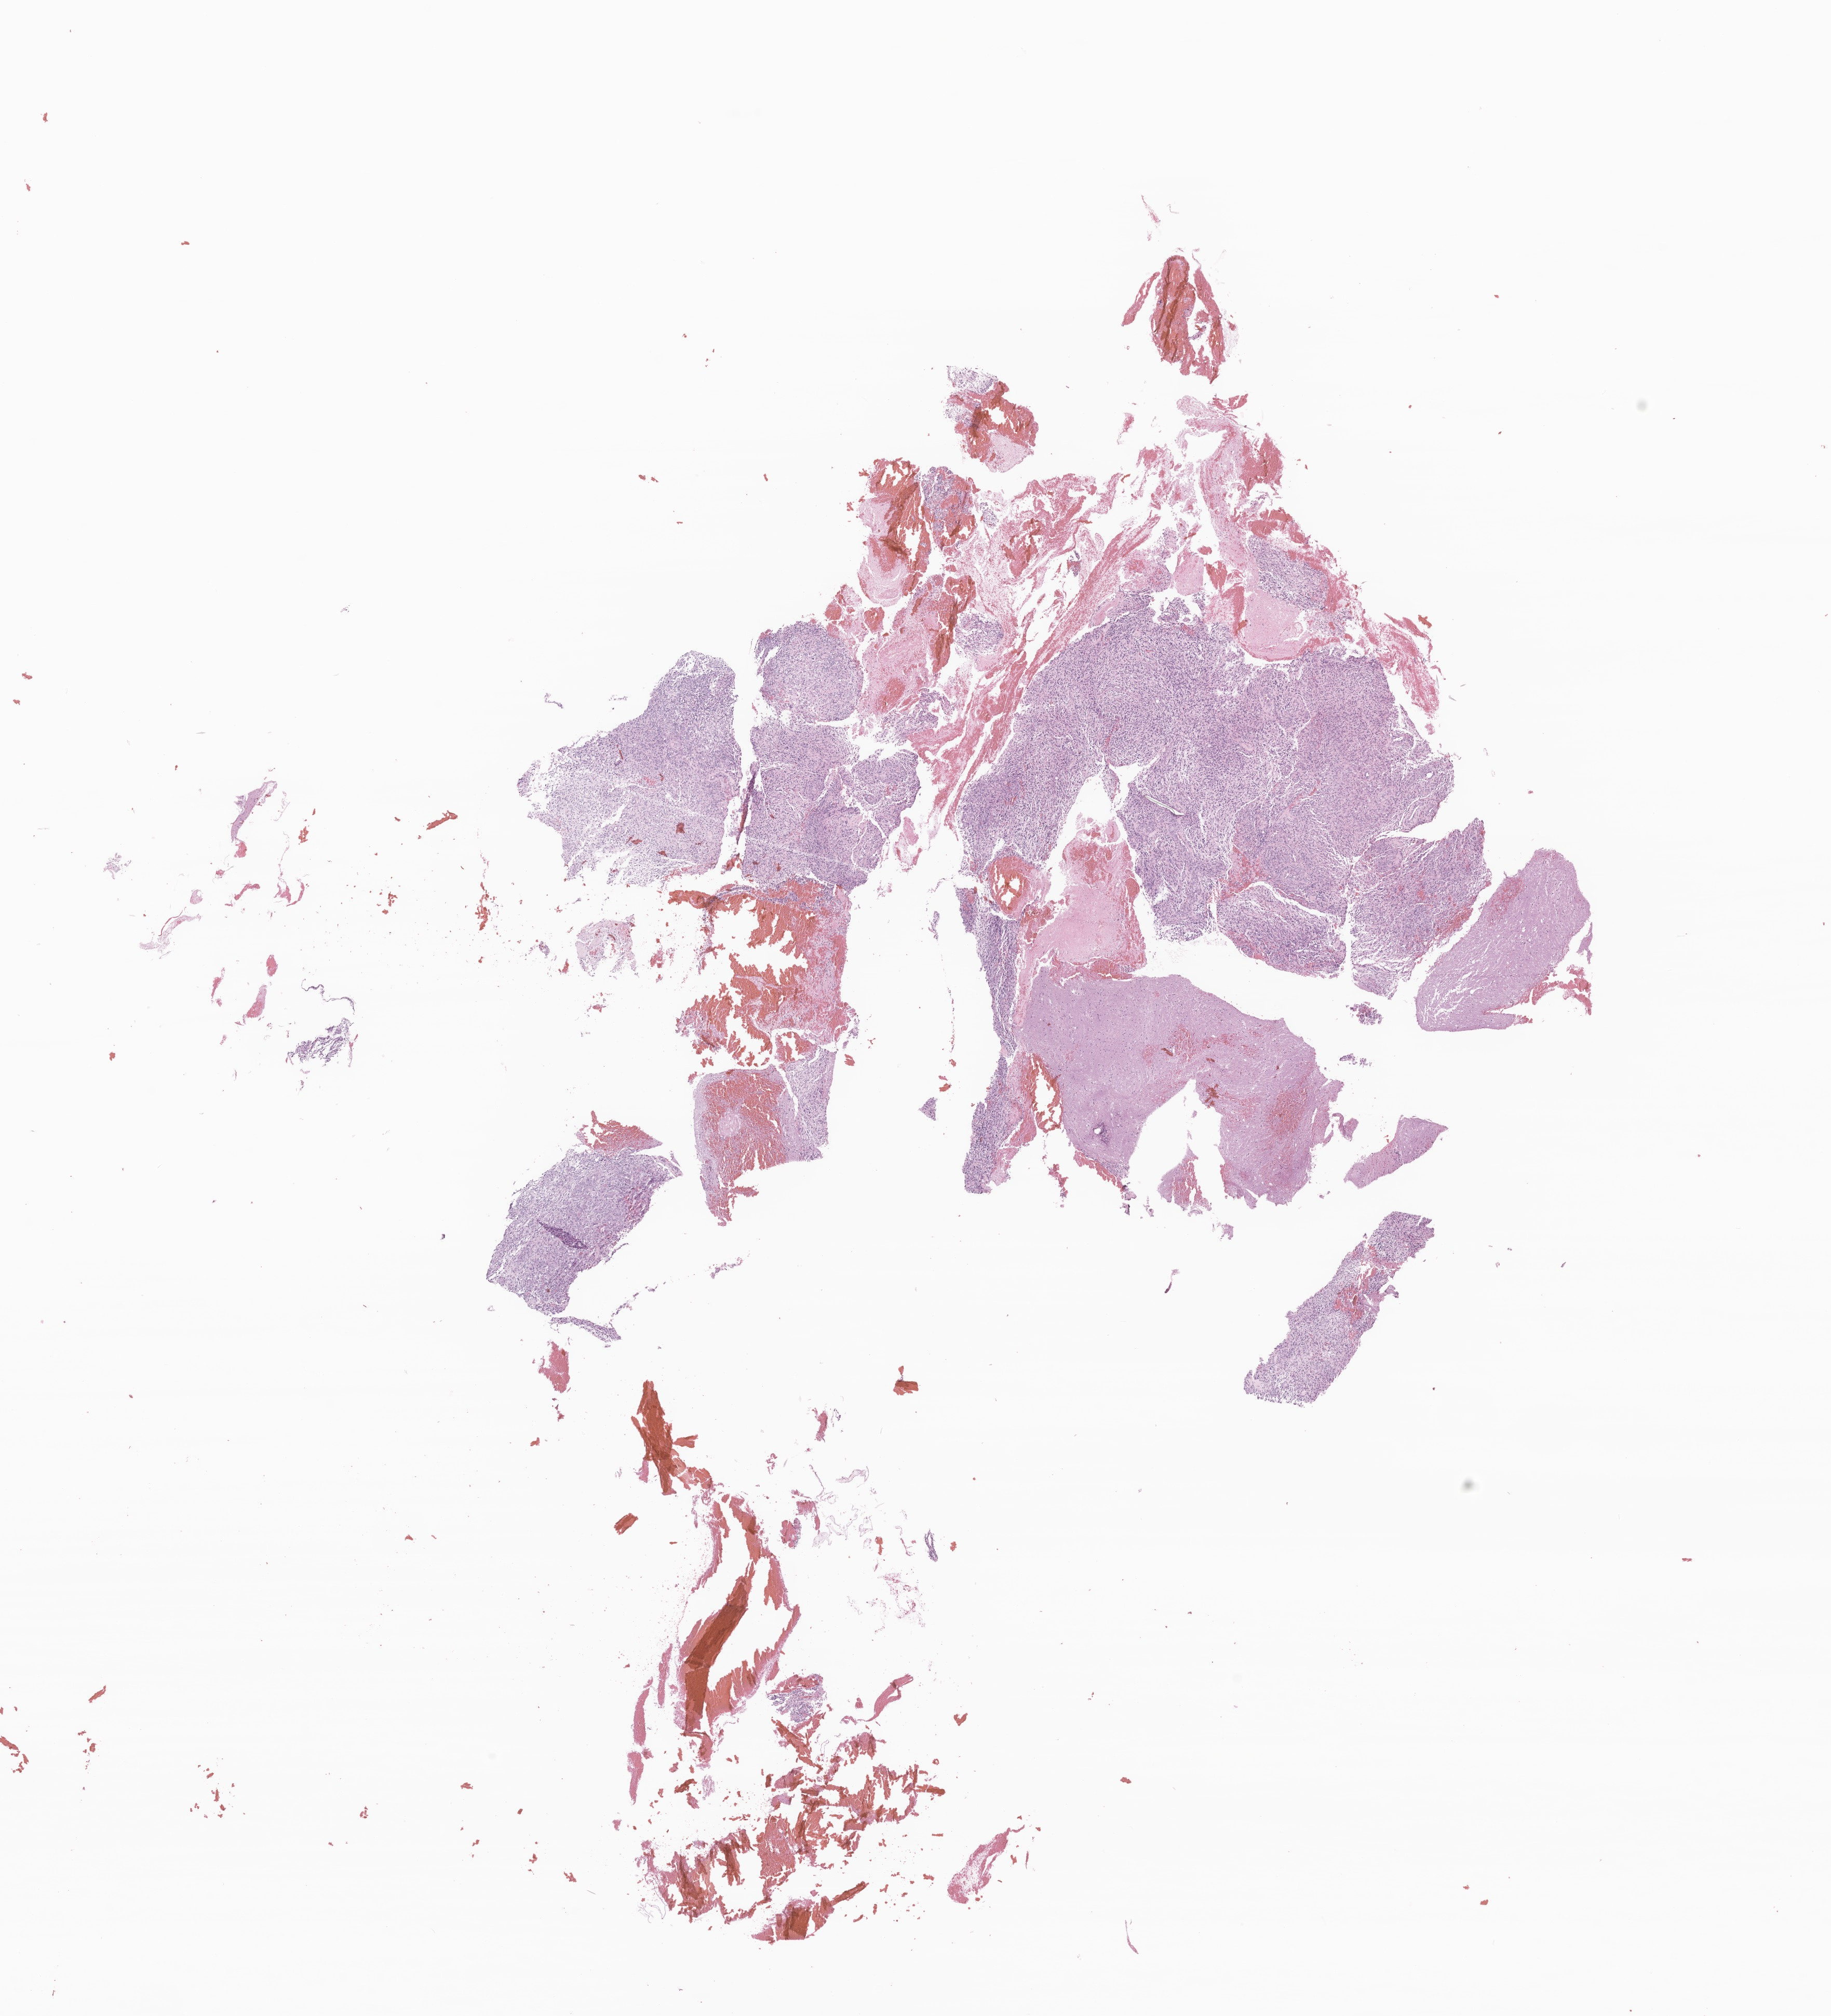
Haematoxylin and eosin whole-slide image of tumor tissue from the brain stem — a low-resolution overview of the entire scanned area, about 14.9 x 16.4 mm; formalin-fixed paraffin-embedded section. Male patient, age 92 months (7 years 8 months).
Diagnosis (ICD-O-3 morphology term): Glioma, malignant.